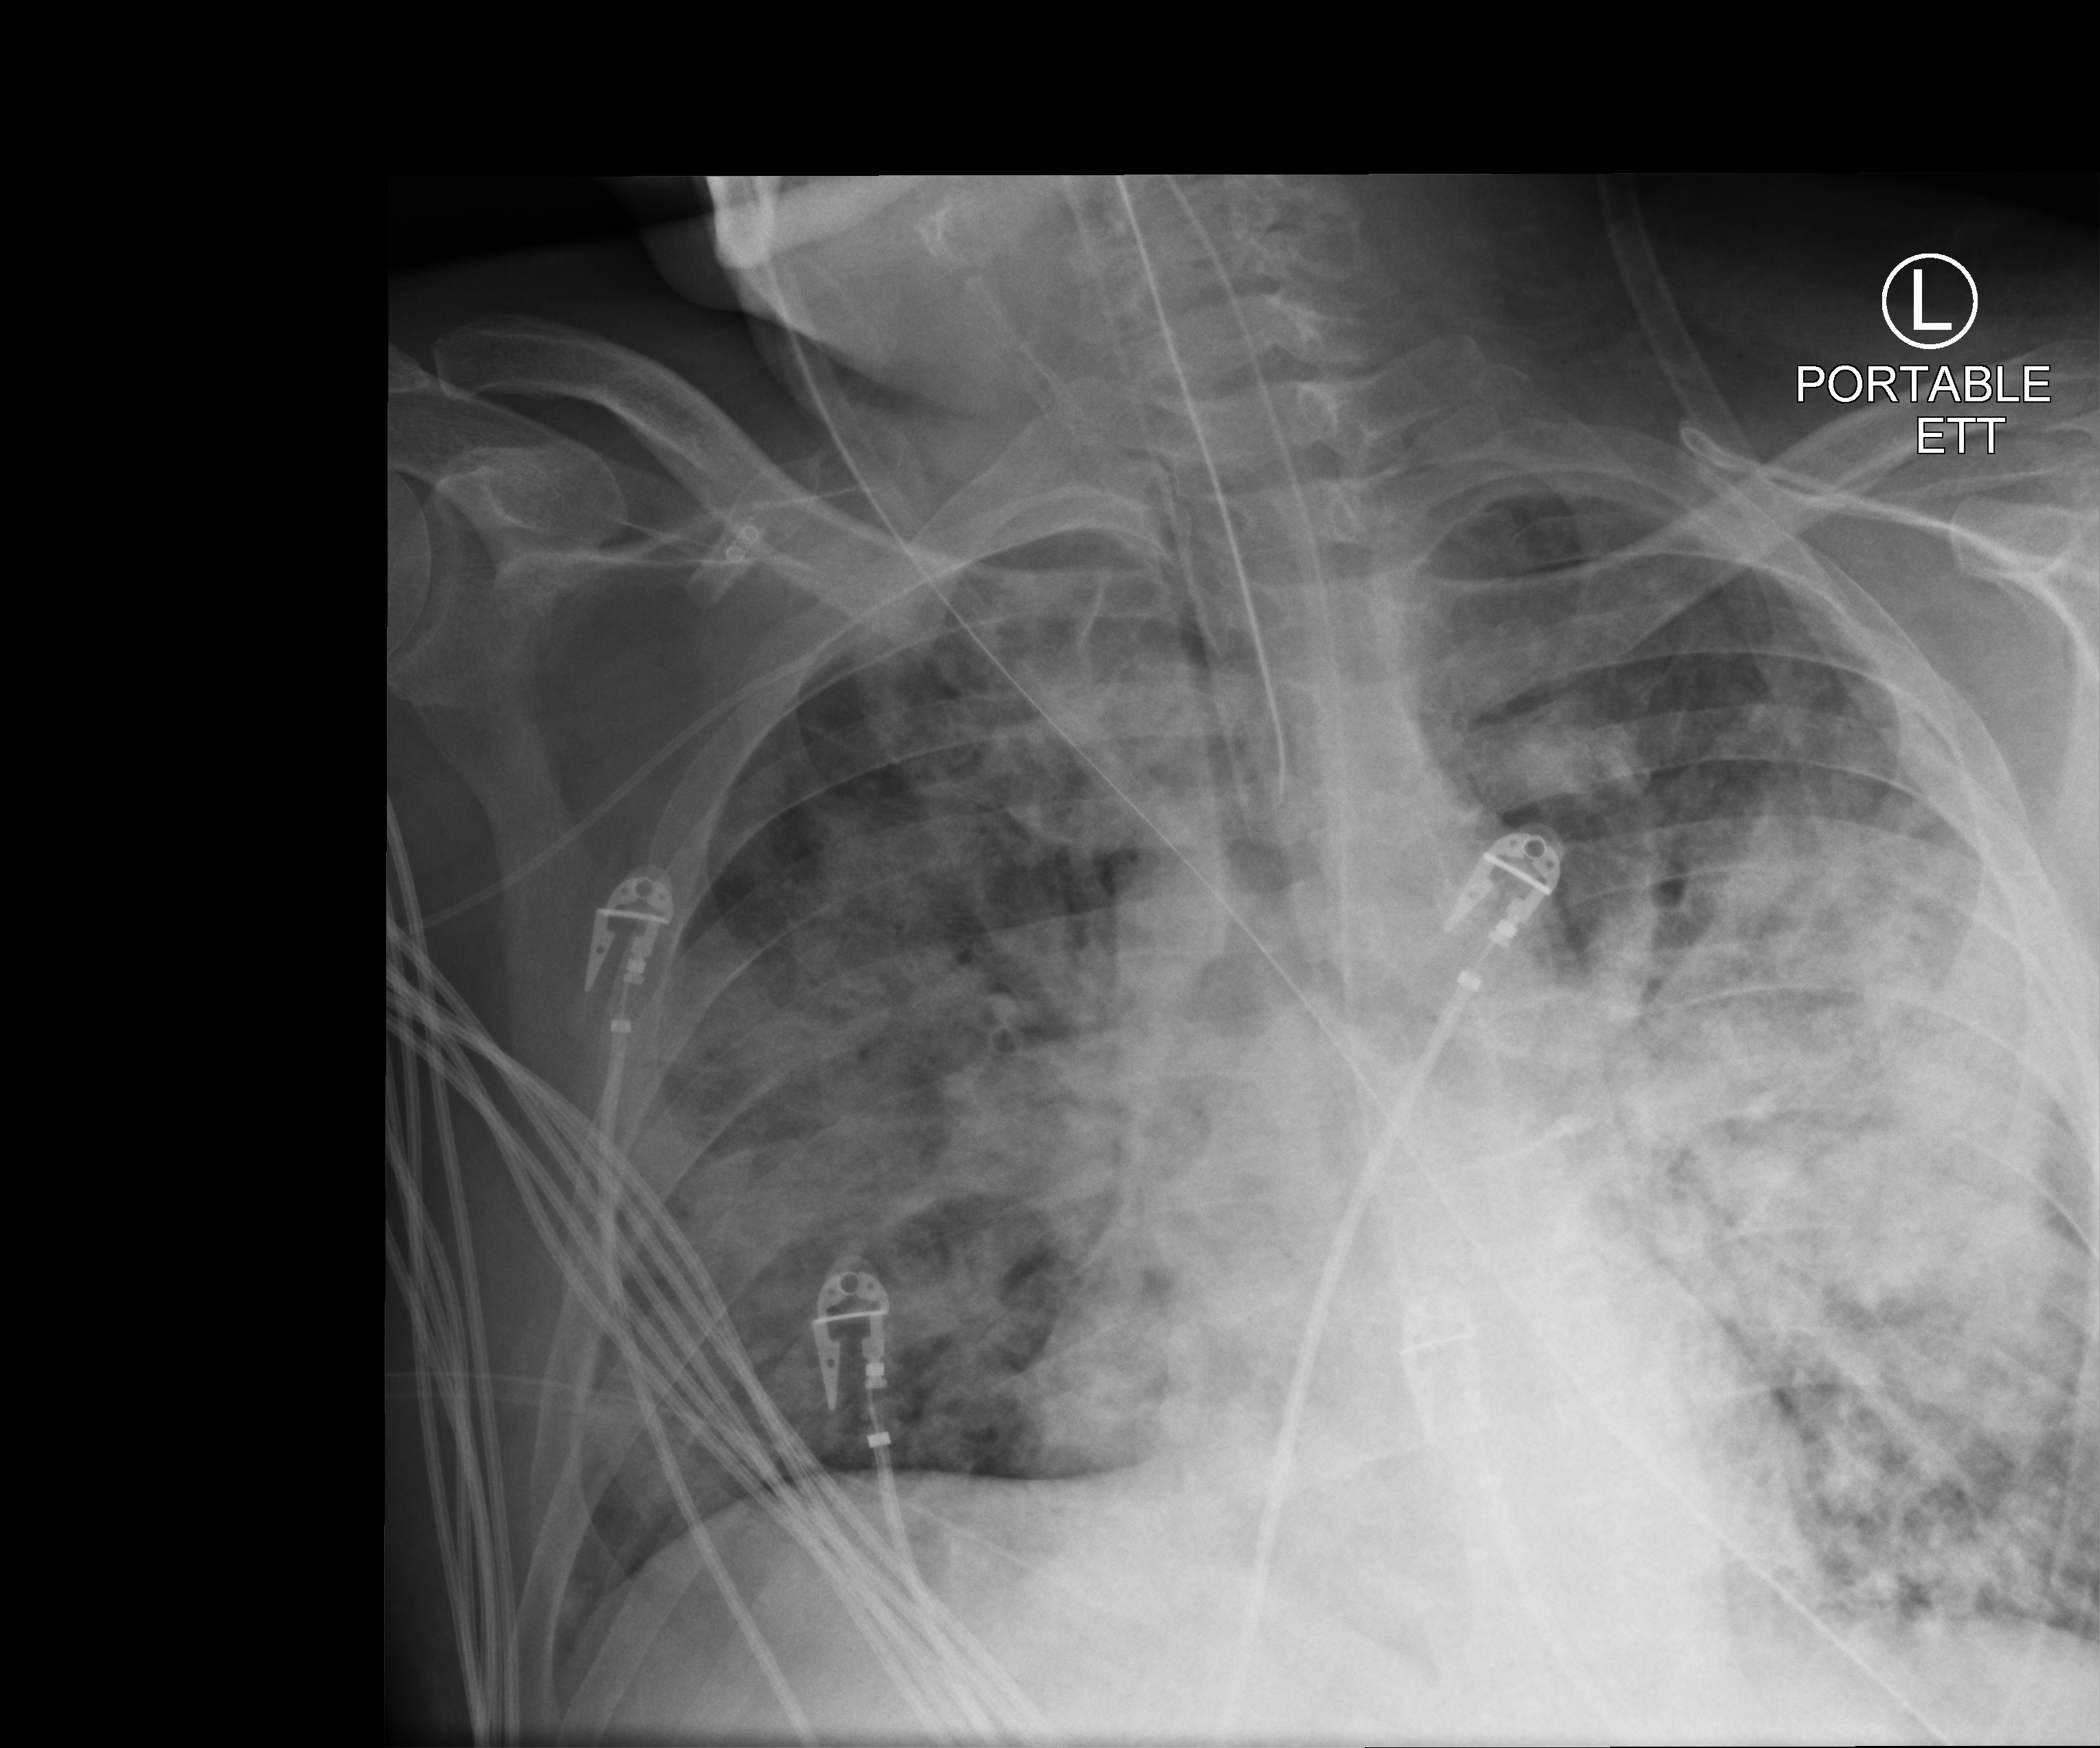
Portable chest radiograph, anteroposterior (AP) projection. Male patient hospitalised with COVID-19, age 18–59 years.
From the hospital-stay record, not from the radiograph (when in the stay this image was taken is not recorded): admitted to intensive care during this hospital stay: yes.